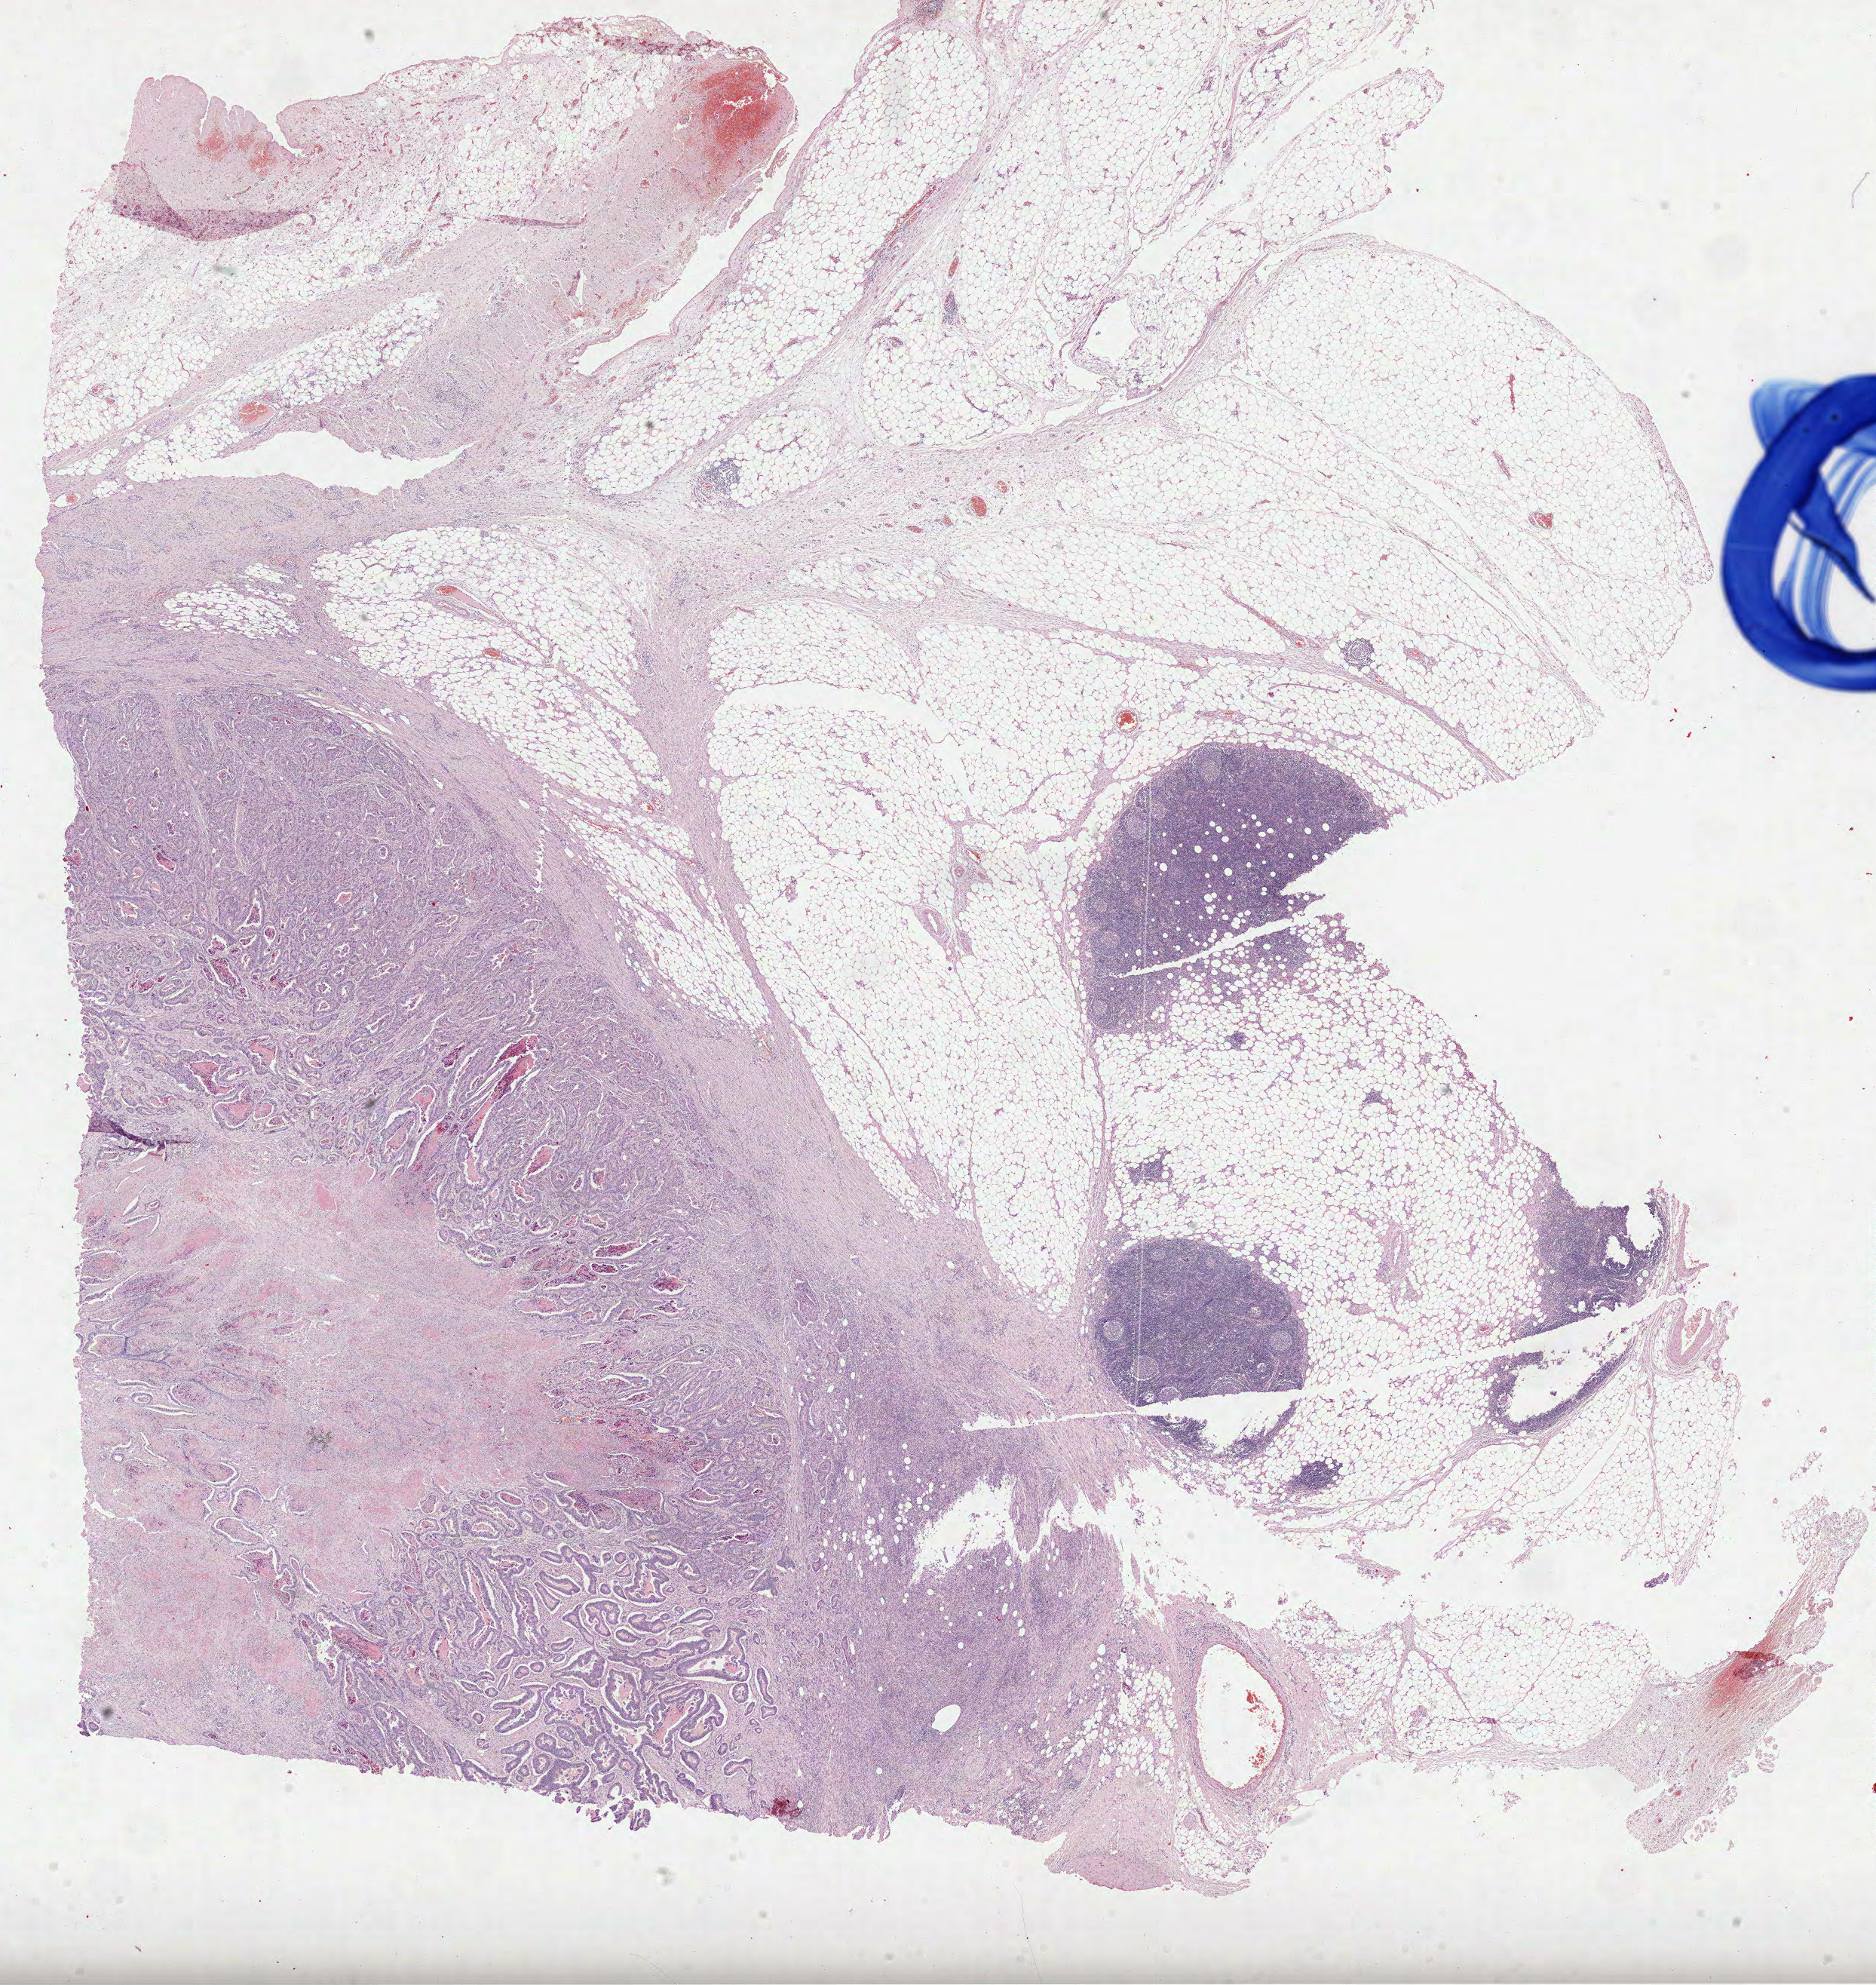
Whole-slide histology image, H&E-stained, a low-resolution overview of the entire scanned area, about 20.1 x 21.2 mm (slide scanned at 40x), FFPE section, primary tumour sample from the stomach. Patient: female, age at initial diagnosis 70 years. Histologic grade: G2 (moderately differentiated).
* lymph nodes positive (case pathology): 0 of 26 examined
* diagnosis: Tubular adenocarcinoma (body of stomach)
* AJCC pathologic stage: IB (6th edition)